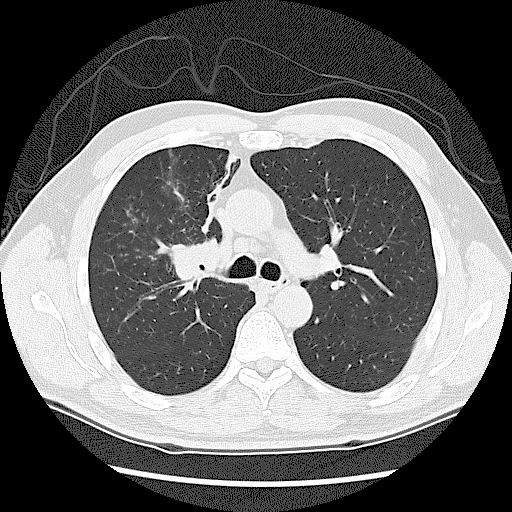
Axial slice from a low-dose chest CT screening exam, baseline screening round, lung window (W 1500 / L -600 HU), 2.5 mm slice thickness, slice 49 of 131 in the series, 512 × 512 image matrix. Male, age 60 years at enrolment. Current smoker at enrolment.
Expert reader's lesion annotation, bounding box <159,222,244,317> (left, top, right, bottom; pixels). Screening reader's record for this exam: no non-calcified nodule ≥4 mm recorded. Official screen result: negative screen, significant abnormalities not suspicious for lung cancer. Participant outcome: lung cancer diagnosed 41 days after this screen — small cell carcinoma, NOS, right upper lobe, stage IIIA (AJCC 6th edition).